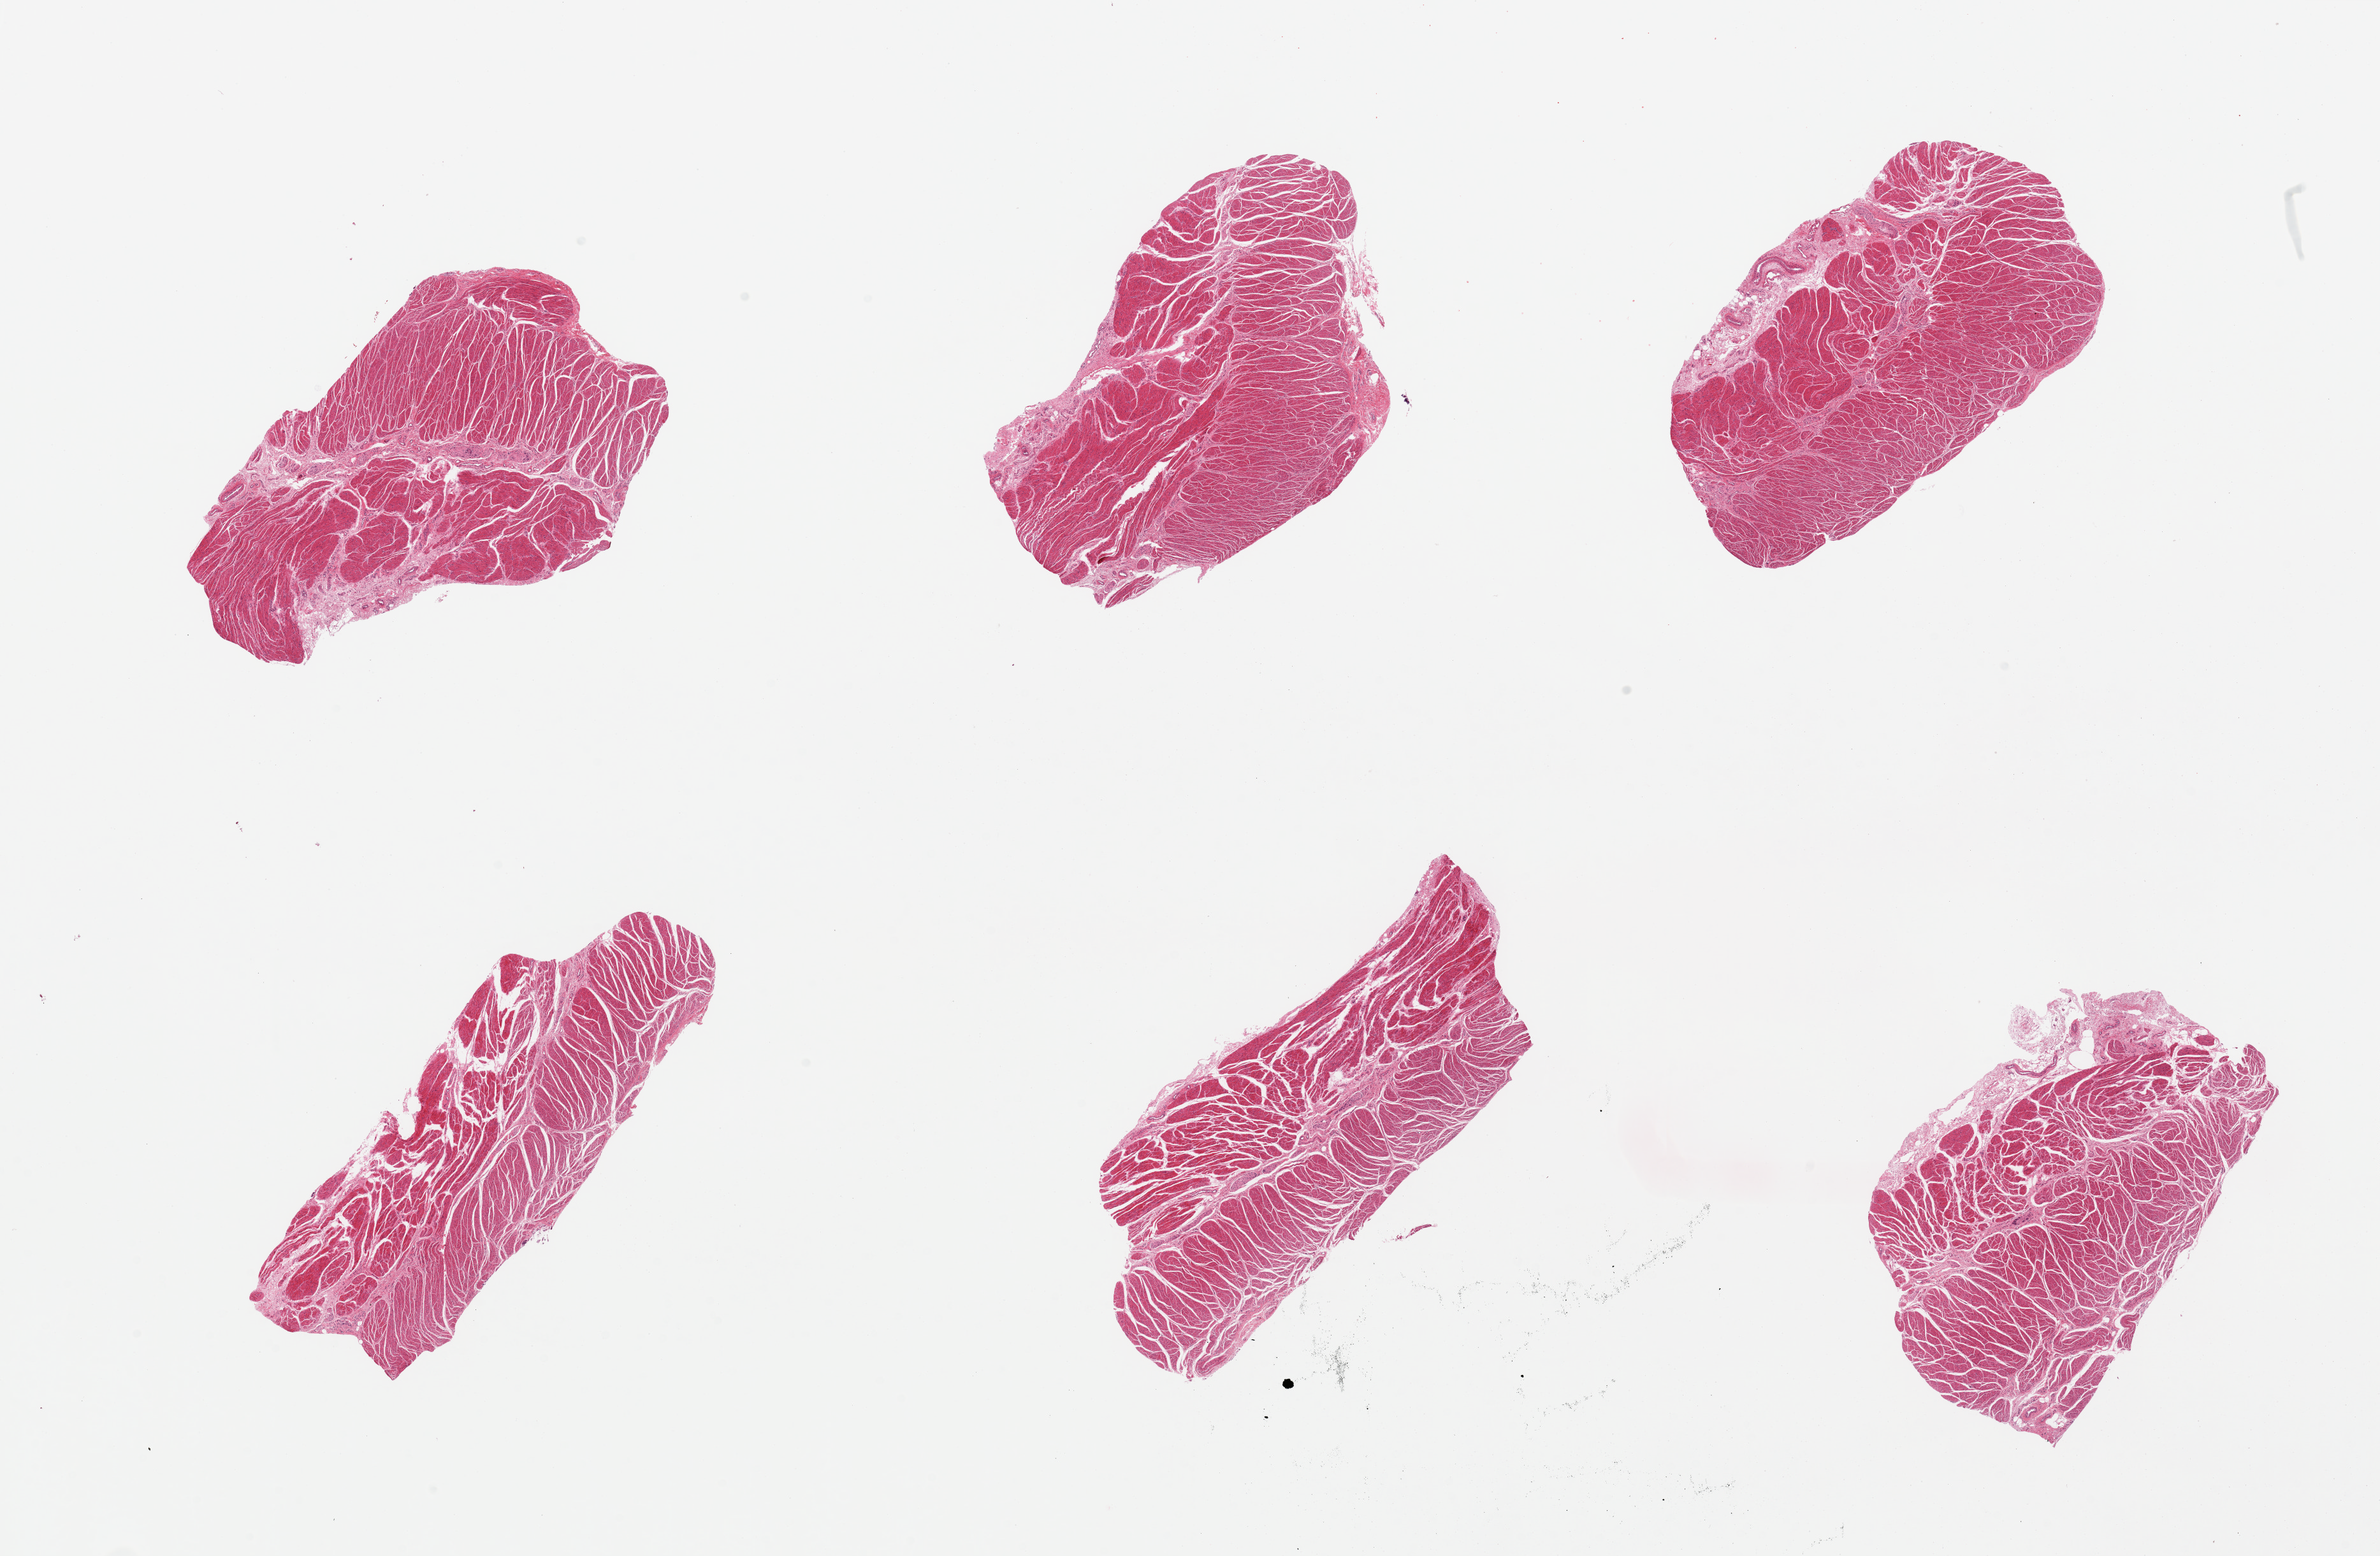
Digitized haematoxylin and eosin-stained section, brightfield, low-resolution overview of the scanned area, about 29.5 x 19.3 mm, PAXgene-fixed, paraffin-embedded tissue, target tissue: esophageal muscle, tissue donor sample. Female donor.
Review note (as recorded): 6 pieces, well trimmed.